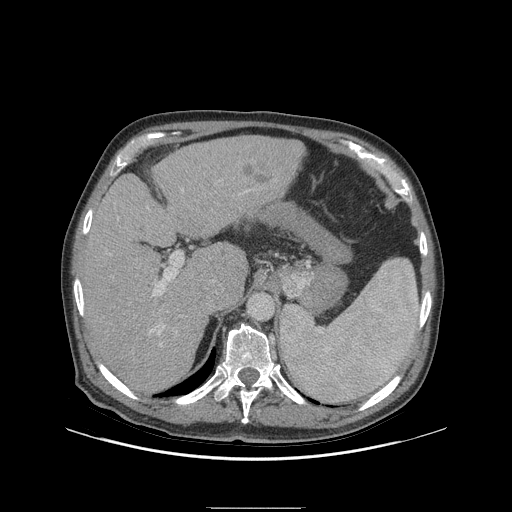
Contrast-enhanced abdominal CT (liver protocol), one axial slice; 140 kVp; soft-tissue window (W 400 / L 40 HU); 2.5 mm slice thickness; 512 × 512 image matrix. From the clinical record (not read from this slice): diagnosis: hepatocellular carcinoma (patient treated with transarterial chemoembolisation; whether this scan precedes or follows treatment is not stated here); TNM stage (as recorded): Stage-I; Child-Pugh class: A.
Structures marked on this image (semi-automatic segmentation, software-assisted and operator-edited):
- liver parenchyma outside the tumour (the mass and vessels are separate outlines, so this box may not span the whole liver): bounding box <80,136,304,393> (left, top, right, bottom; pixels)
- mass: <242,146,282,181>
- liver vessels: <117,180,250,346>